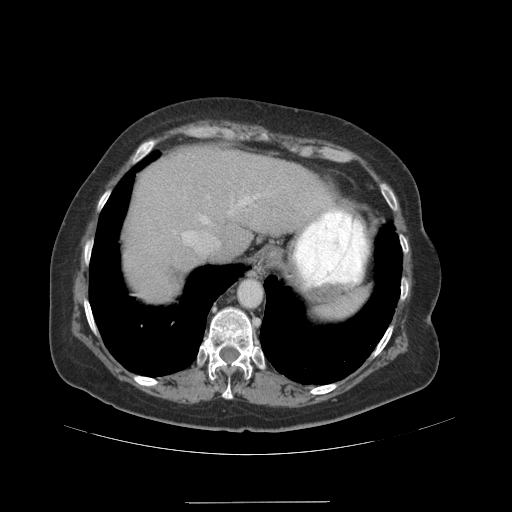
Contrast-enhanced abdominal CT (liver protocol), one axial slice; soft-tissue window (W 400 / L 40 HU); 512 × 512 image matrix, field of view 440 × 440 mm. Case-level facts recorded for this patient, not image findings: diagnosis: hepatocellular carcinoma (patient treated with transarterial chemoembolisation; whether this scan precedes or follows treatment is not stated here); TNM stage (as recorded): Stage-IVA; Child-Pugh class: A.
Outlined on this slice (semi-automatic segmentation, software-assisted and operator-edited):
- abdominal aorta: bounding box <238,280,261,308> (left, top, right, bottom; pixels)
- liver parenchyma outside the tumour (the mass and vessels are separate outlines, so this box may not span the whole liver): <124,146,332,300>
- liver vessels: <182,194,260,250>